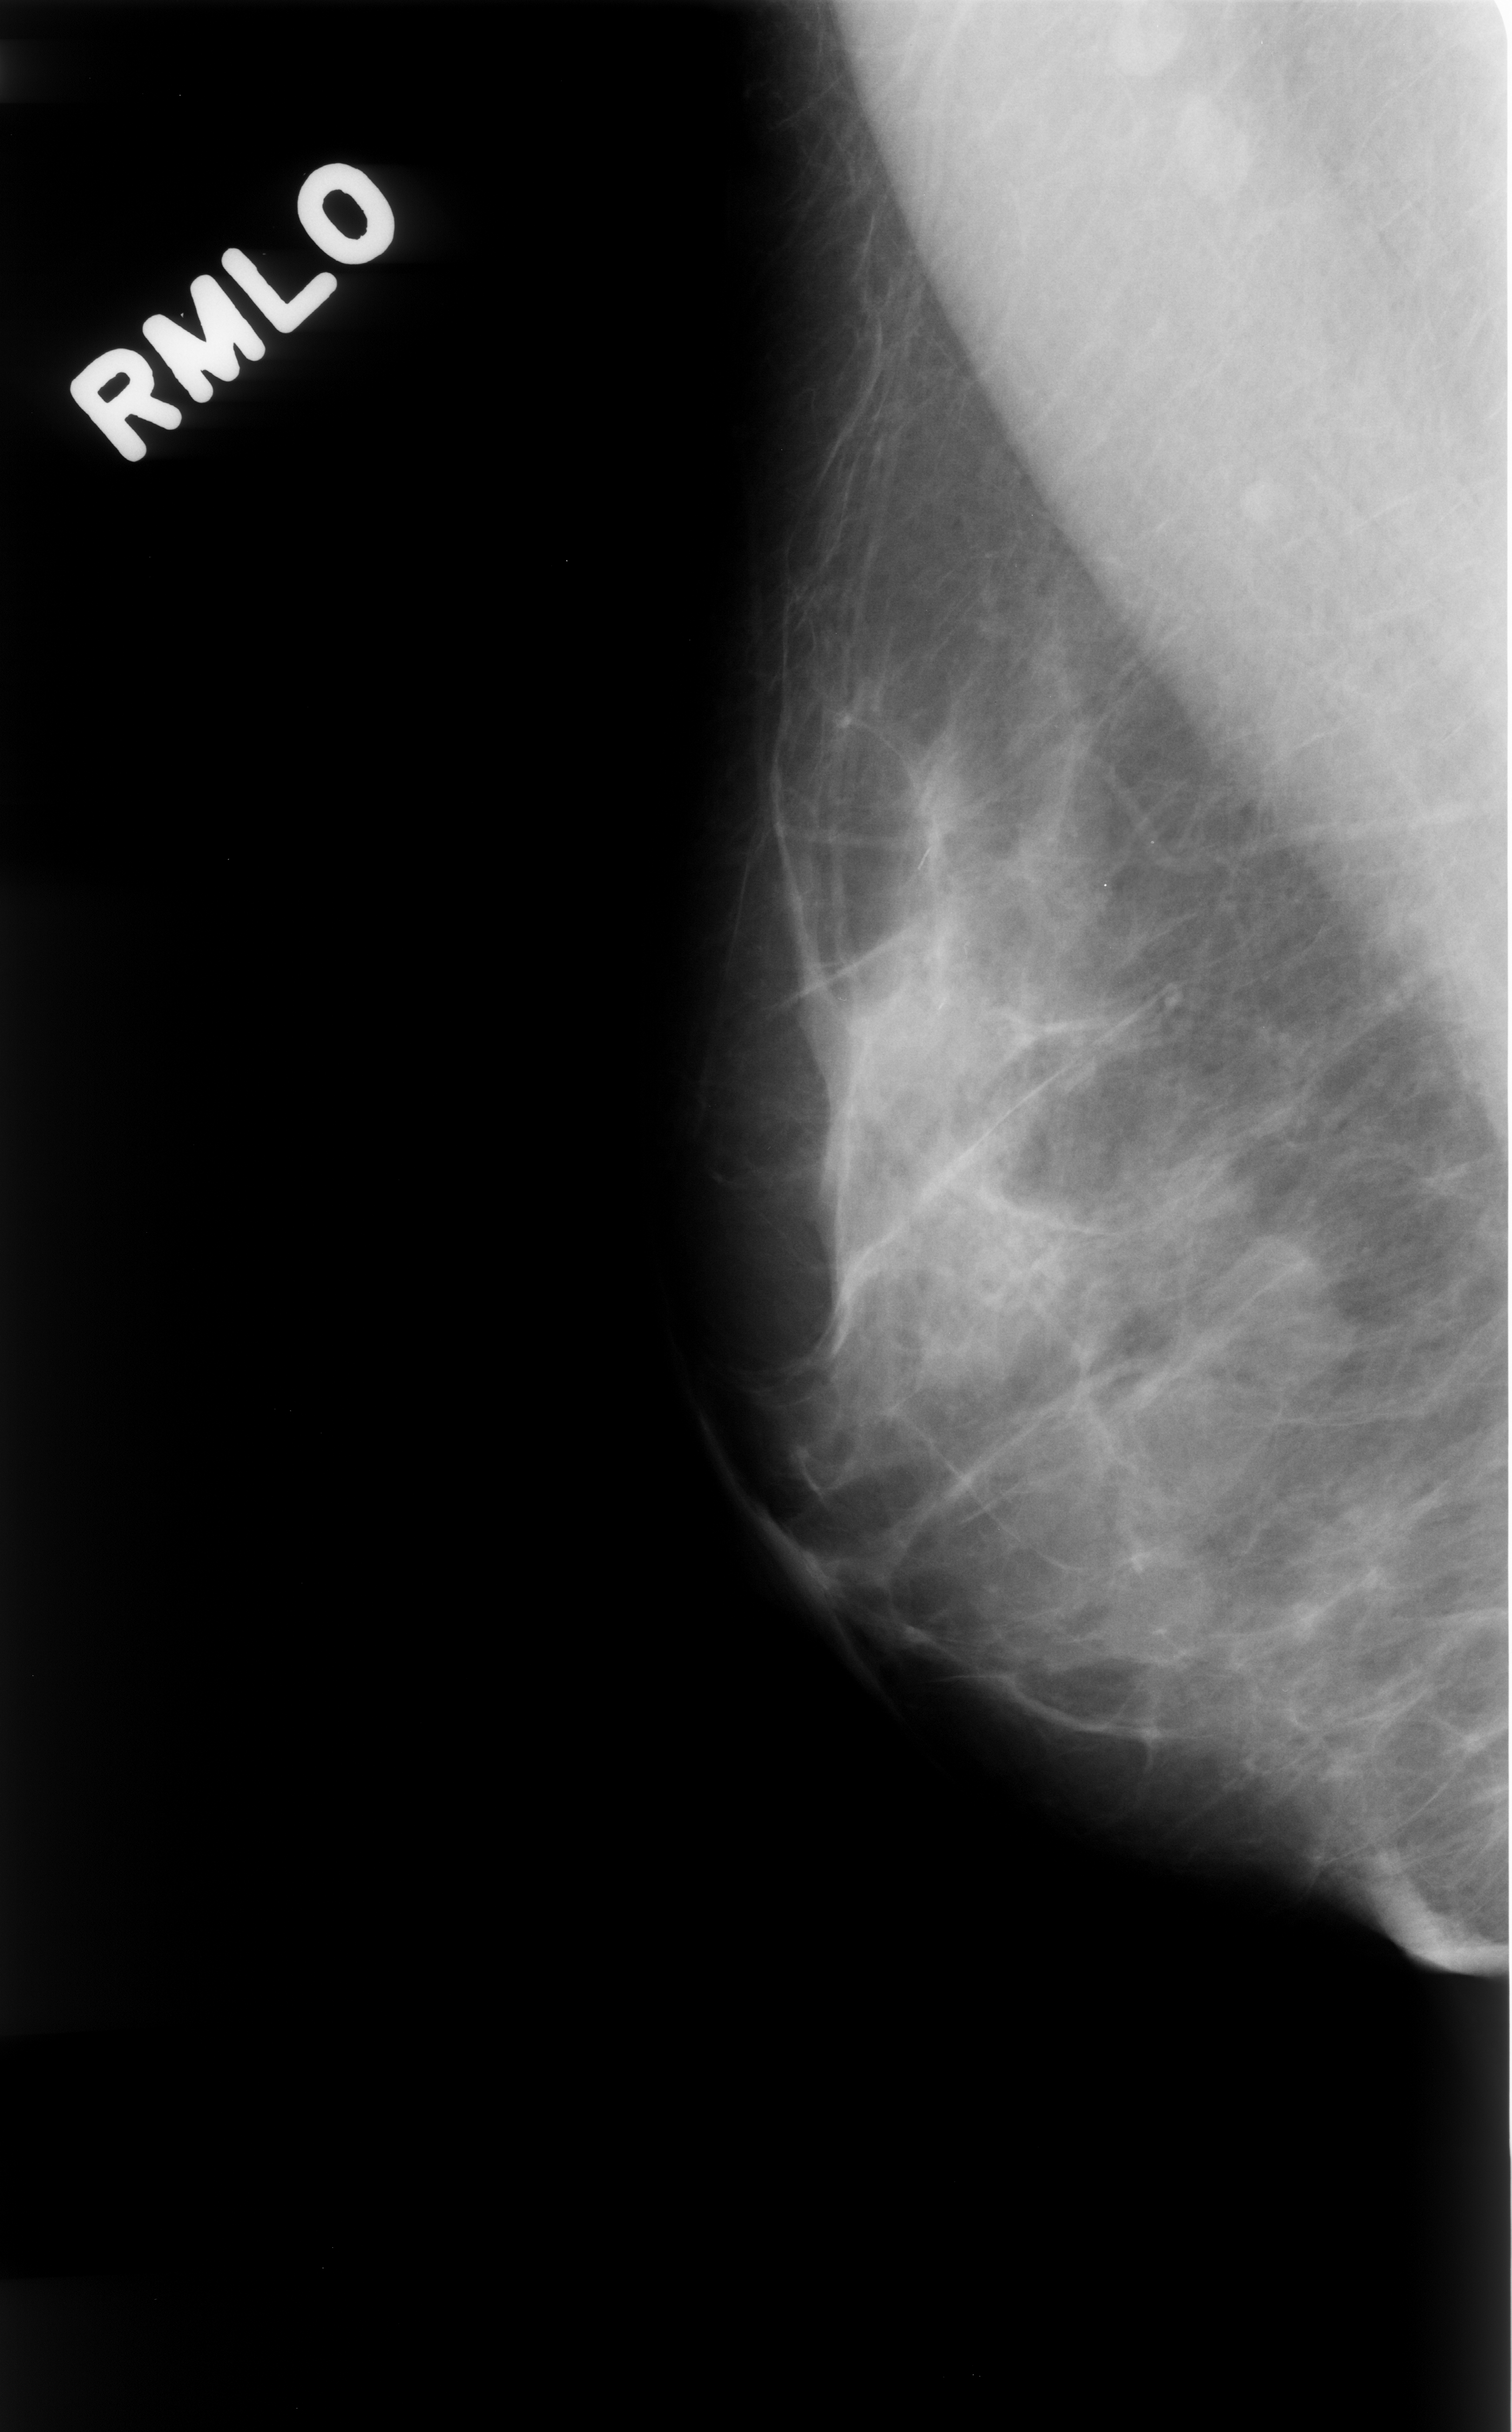
Scanned film-screen mammogram, right breast, mediolateral oblique (MLO) view, breast composition: scattered fibroglandular densities (BI-RADS density category 2 of 4).
- Radiologist-marked abnormalities on this image: calcifications, morphology fine linear branching, distribution linear; BI-RADS assessment category 4; subtlety rating 4 on a 1 (subtle) to 5 (obvious) scale; pathology (as recorded): benign.